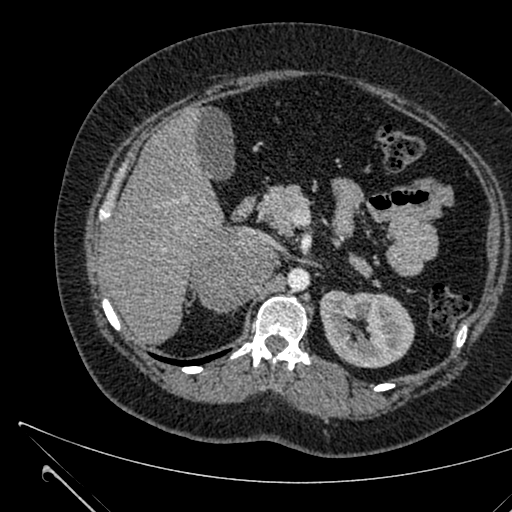
Contrast-enhanced abdominal CT, one axial slice. Position 403 of 731 along the scan axis. 120 kVp. Intravenous contrast given. Soft-tissue window (W 400 / L 40 HU). 1 mm slice thickness. 512 × 512 image matrix. Female patient, age 36 years. Case-level facts recorded for this patient, not image findings: diagnosis: adrenocortical carcinoma; tumour side: right adrenal; tumour size at pathology: 10 cm; Ki-67 index: 20 %.
Outlined on this slice (semi-automatic segmentation, software-assisted and operator-edited):
- mass: bounding box <194,227,277,310> (left, top, right, bottom; pixels)